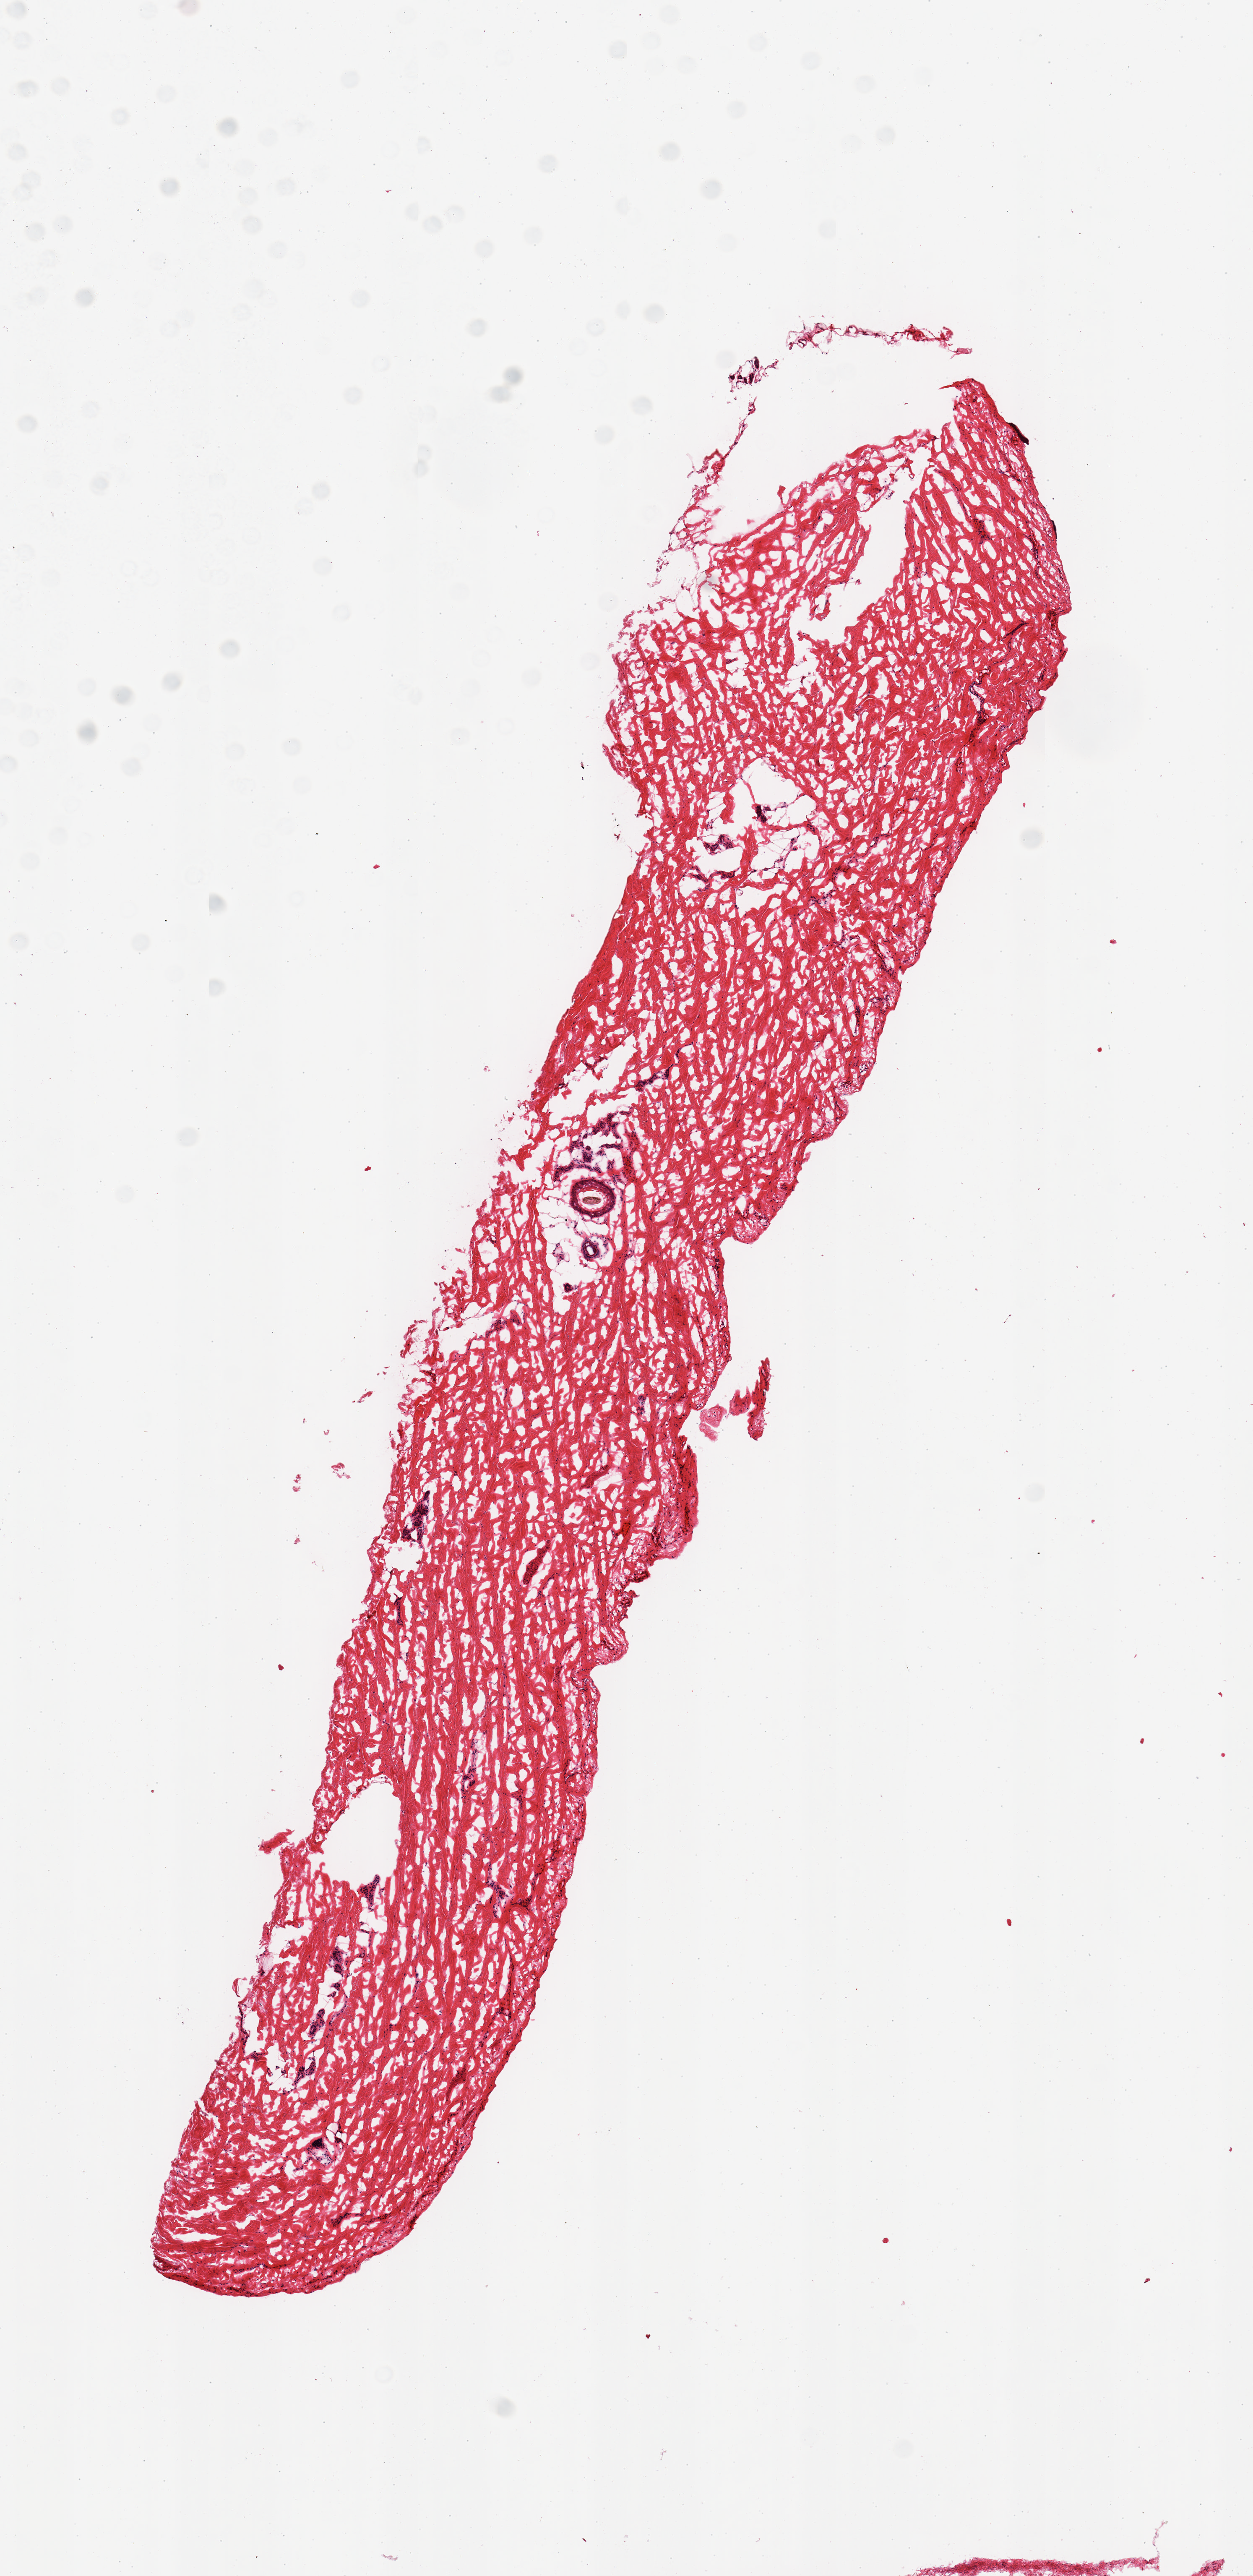
Haematoxylin and eosin whole-slide image, brightfield — whole scanned area (about 5.9 x 12.1 mm, from a 20x scan) shown as a low-resolution overview; frozen section (dry ice); section of skin of lower leg (target tissue); donor tissue sample. Donor sex: female.
Reviewer comment on this tissue sample: 1 piece; only focal epidermis.